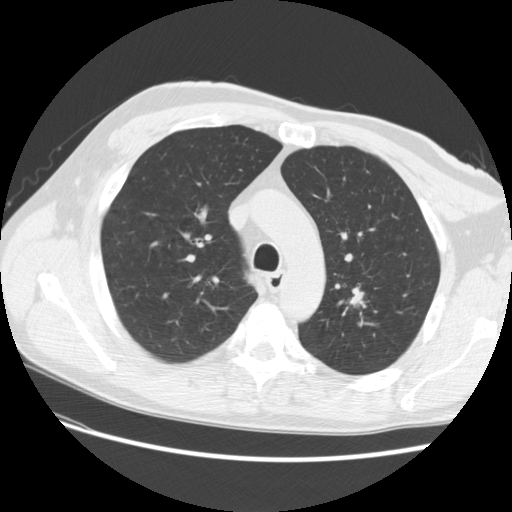
Low-dose screening chest CT, one axial slice; position 187 of 256 along the scan axis; lung window (W 1500 / L -600 HU); 512 × 512 image matrix, field of view 366 × 366 mm.
Outlined on this slice (manually delineated by an expert):
- lesion 1 (tumor, upper lobe of left lung): box from (x=350, y=292) to (x=364, y=305) px